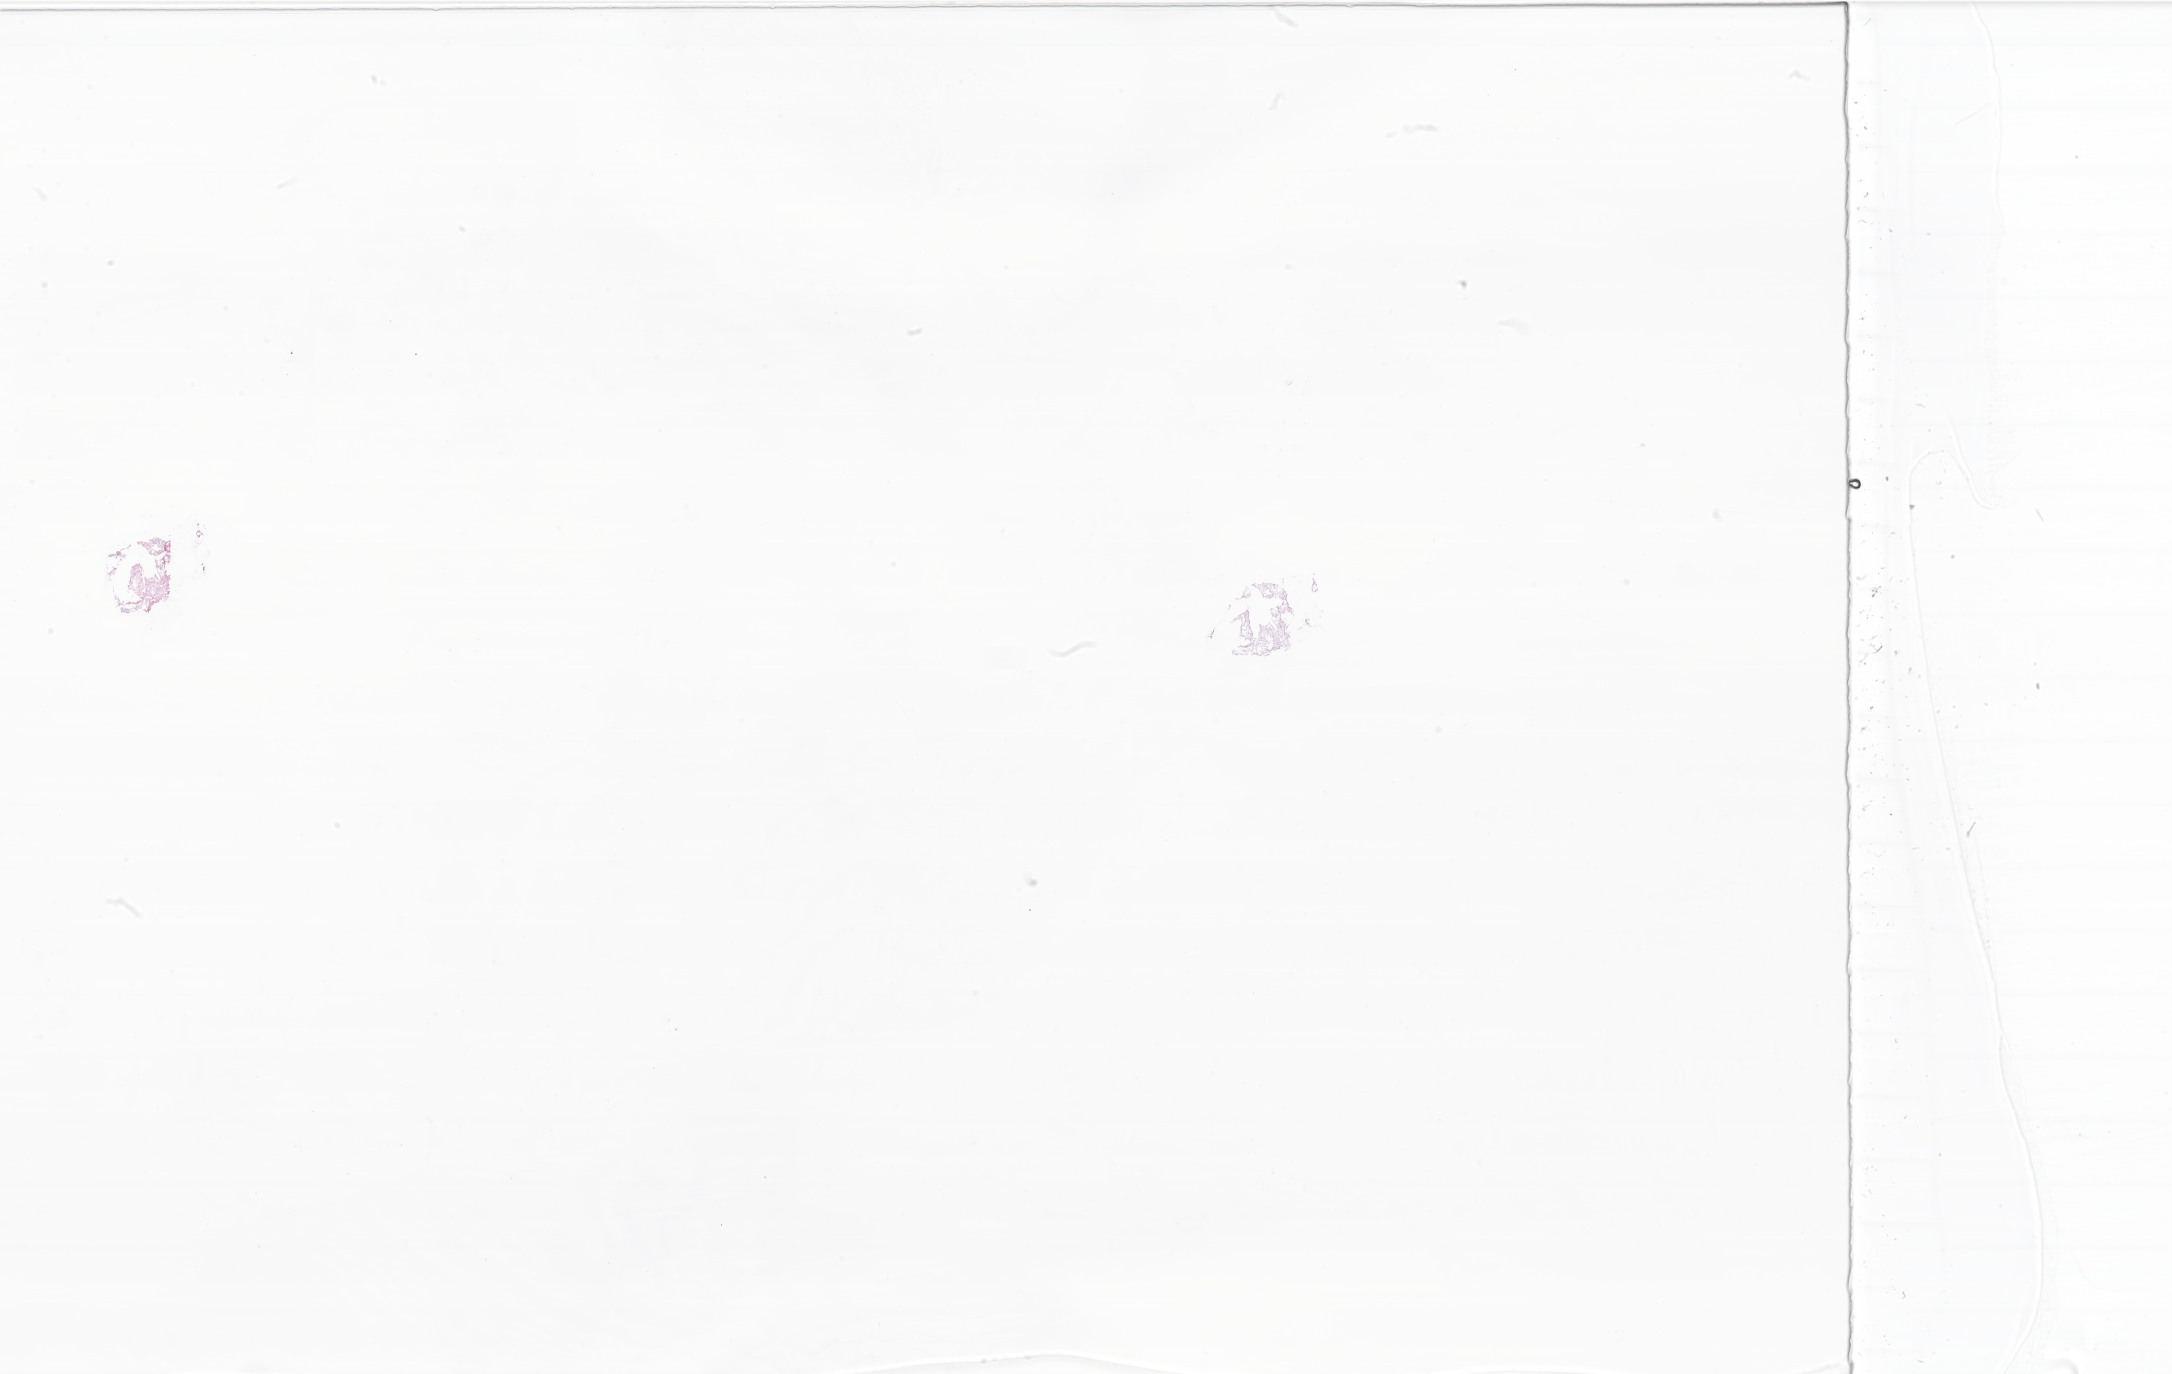
Whole-slide image, haematoxylin and eosin stain of tumor tissue from the frontal lobe — whole scanned area (about 36.6 x 23.2 mm) shown as a low-resolution overview, frozen section. Patient: male, age 163 days.
Diagnosis: Neoplasm, metastatic.